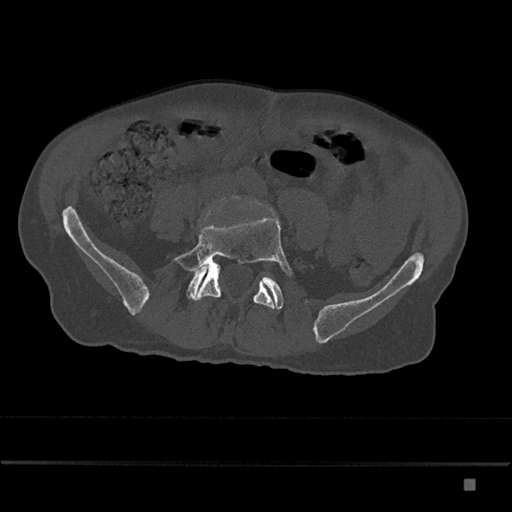
CT including the spine, one axial slice. Slice 275 of 797 in the series (ordered by position). Reconstruction kernel Br40s/3. 120 kVp. Bone window (W 1800 / L 400 HU). 512 × 512 image matrix, field of view 390 × 390 mm. Male patient, age 72 years. From the clinical record (not read from this slice): primary cancer: prostate.
Annotated regions visible in this slice (semi-automatic segmentation, software-assisted and operator-edited):
- L5 vertebra: bounding box [x1, y1, x2, y2] px = [171, 205, 293, 309]